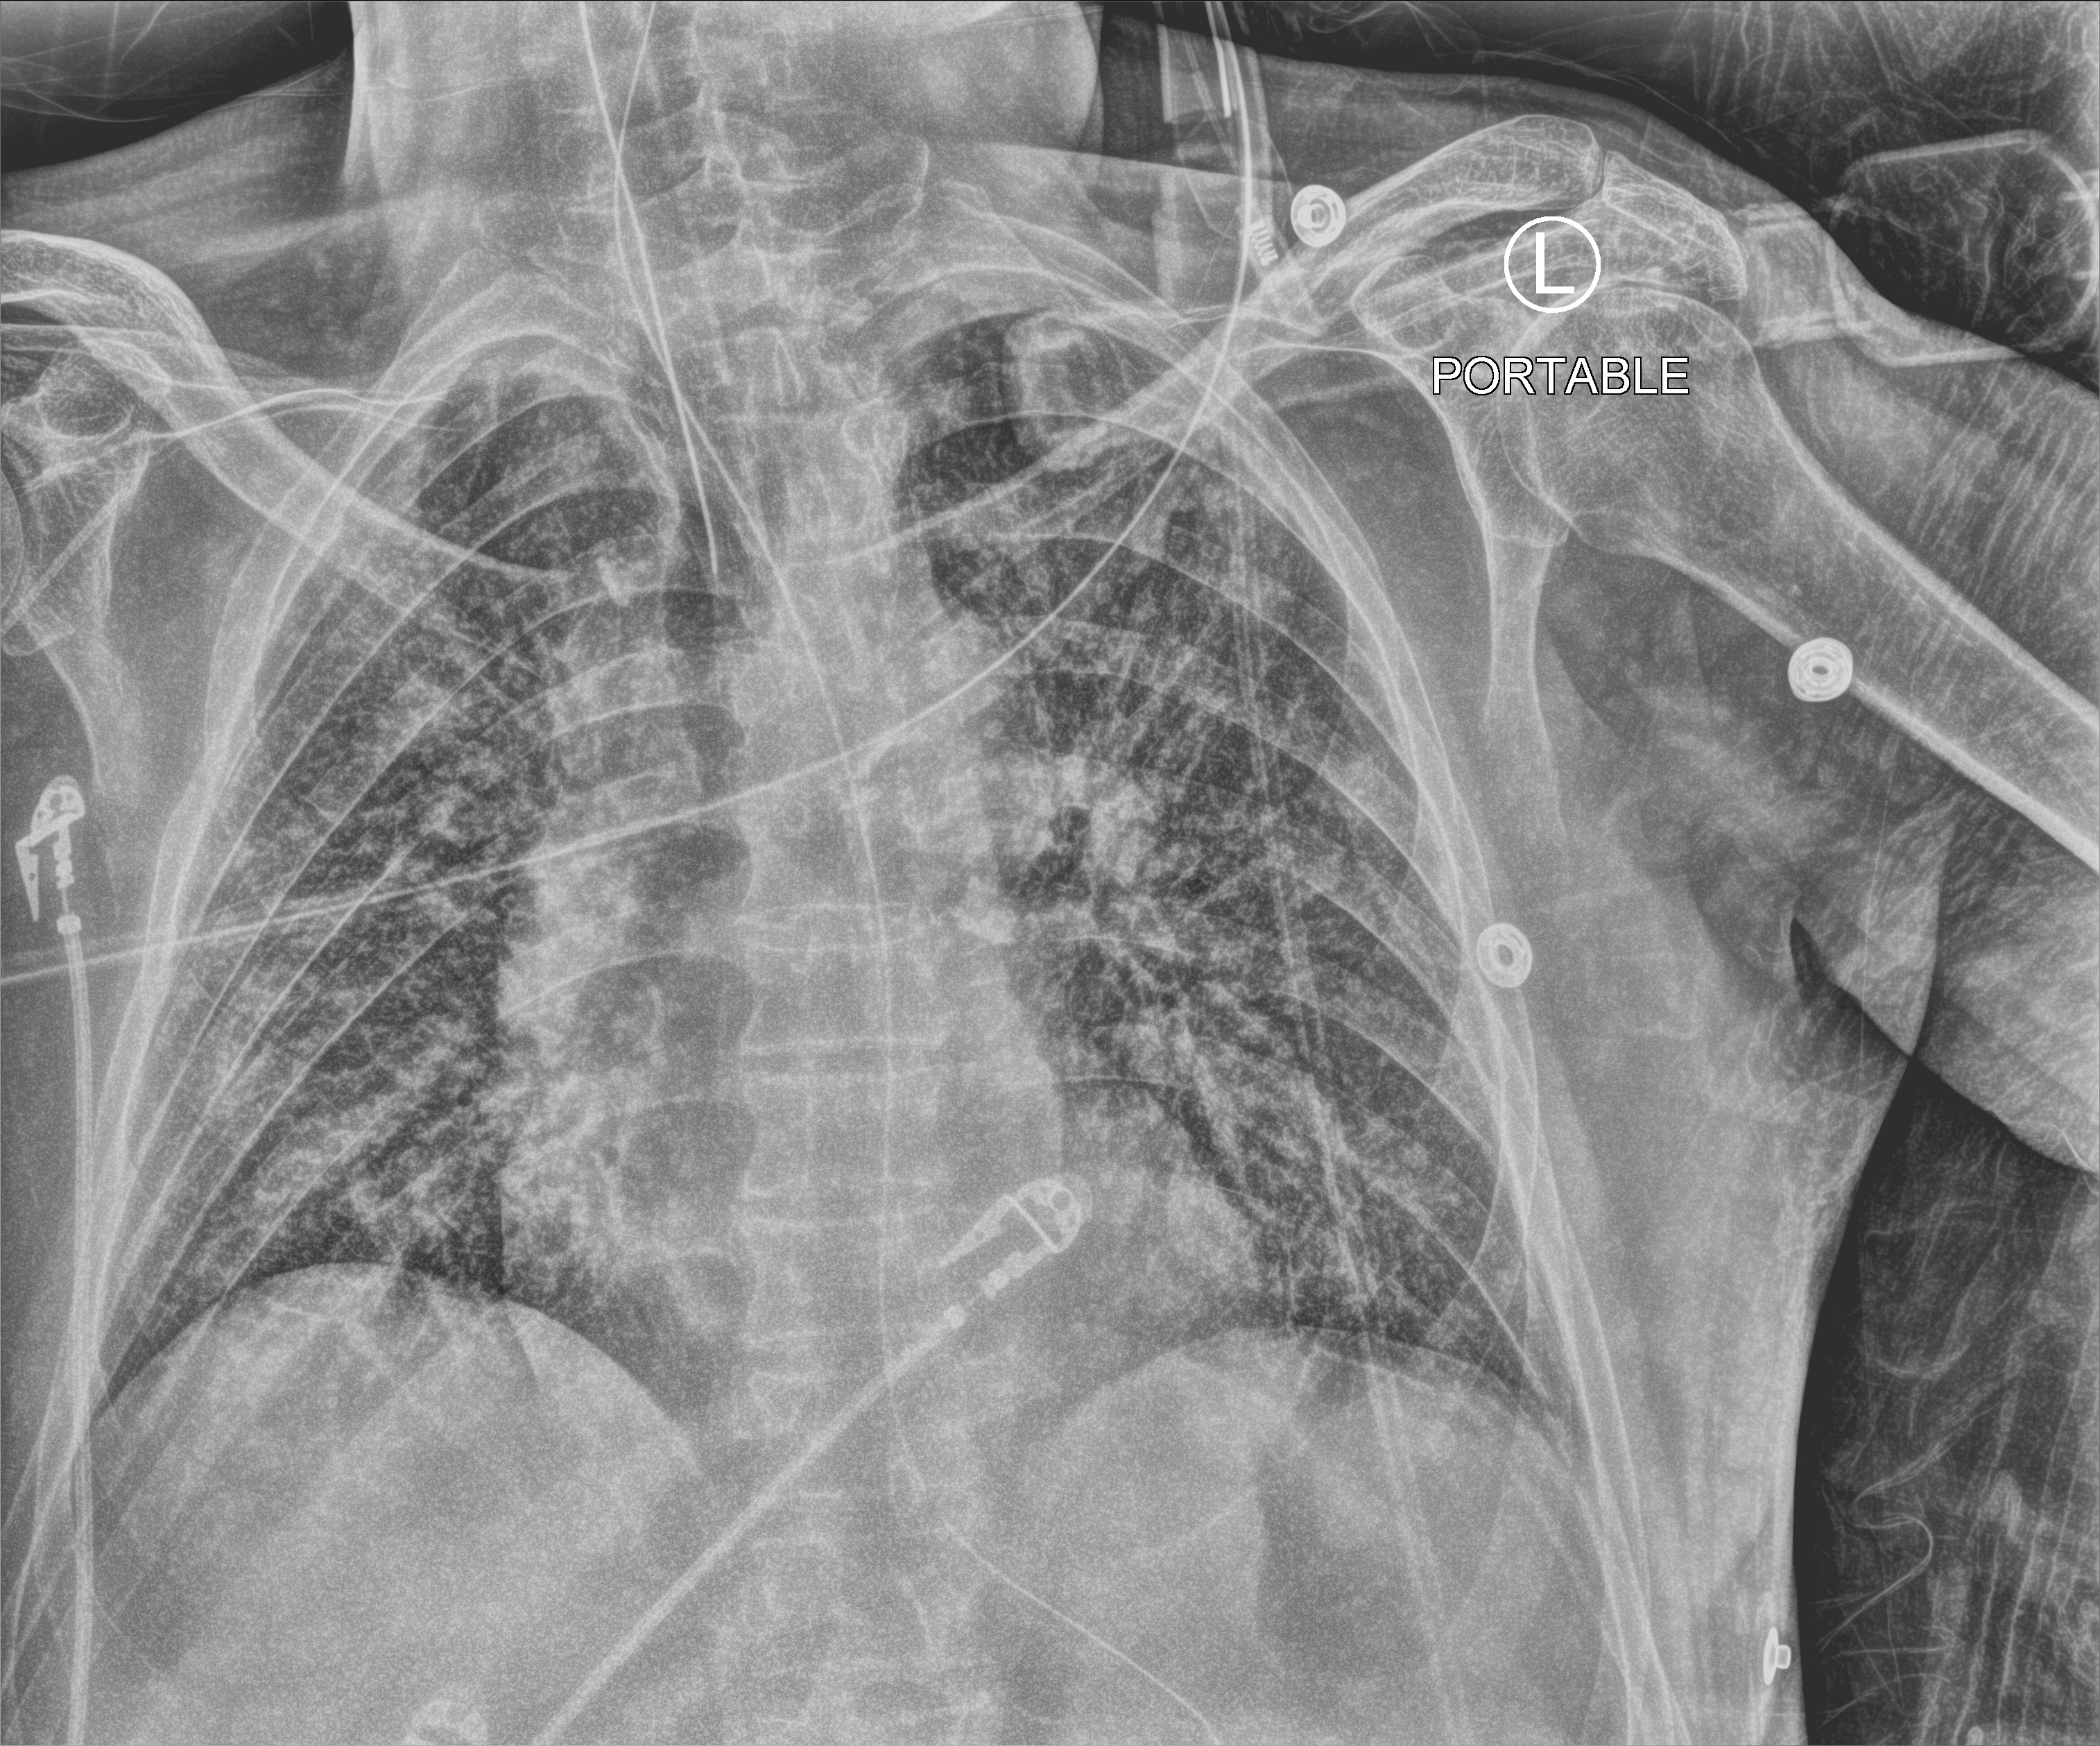
Bedside chest radiograph (computed radiography). Male patient hospitalised with COVID-19, age 60–74 years.
From the hospital-stay record, not from the radiograph (when in the stay this image was taken is not recorded): length of hospital stay: 25 days; admitted to intensive care during this hospital stay: yes.